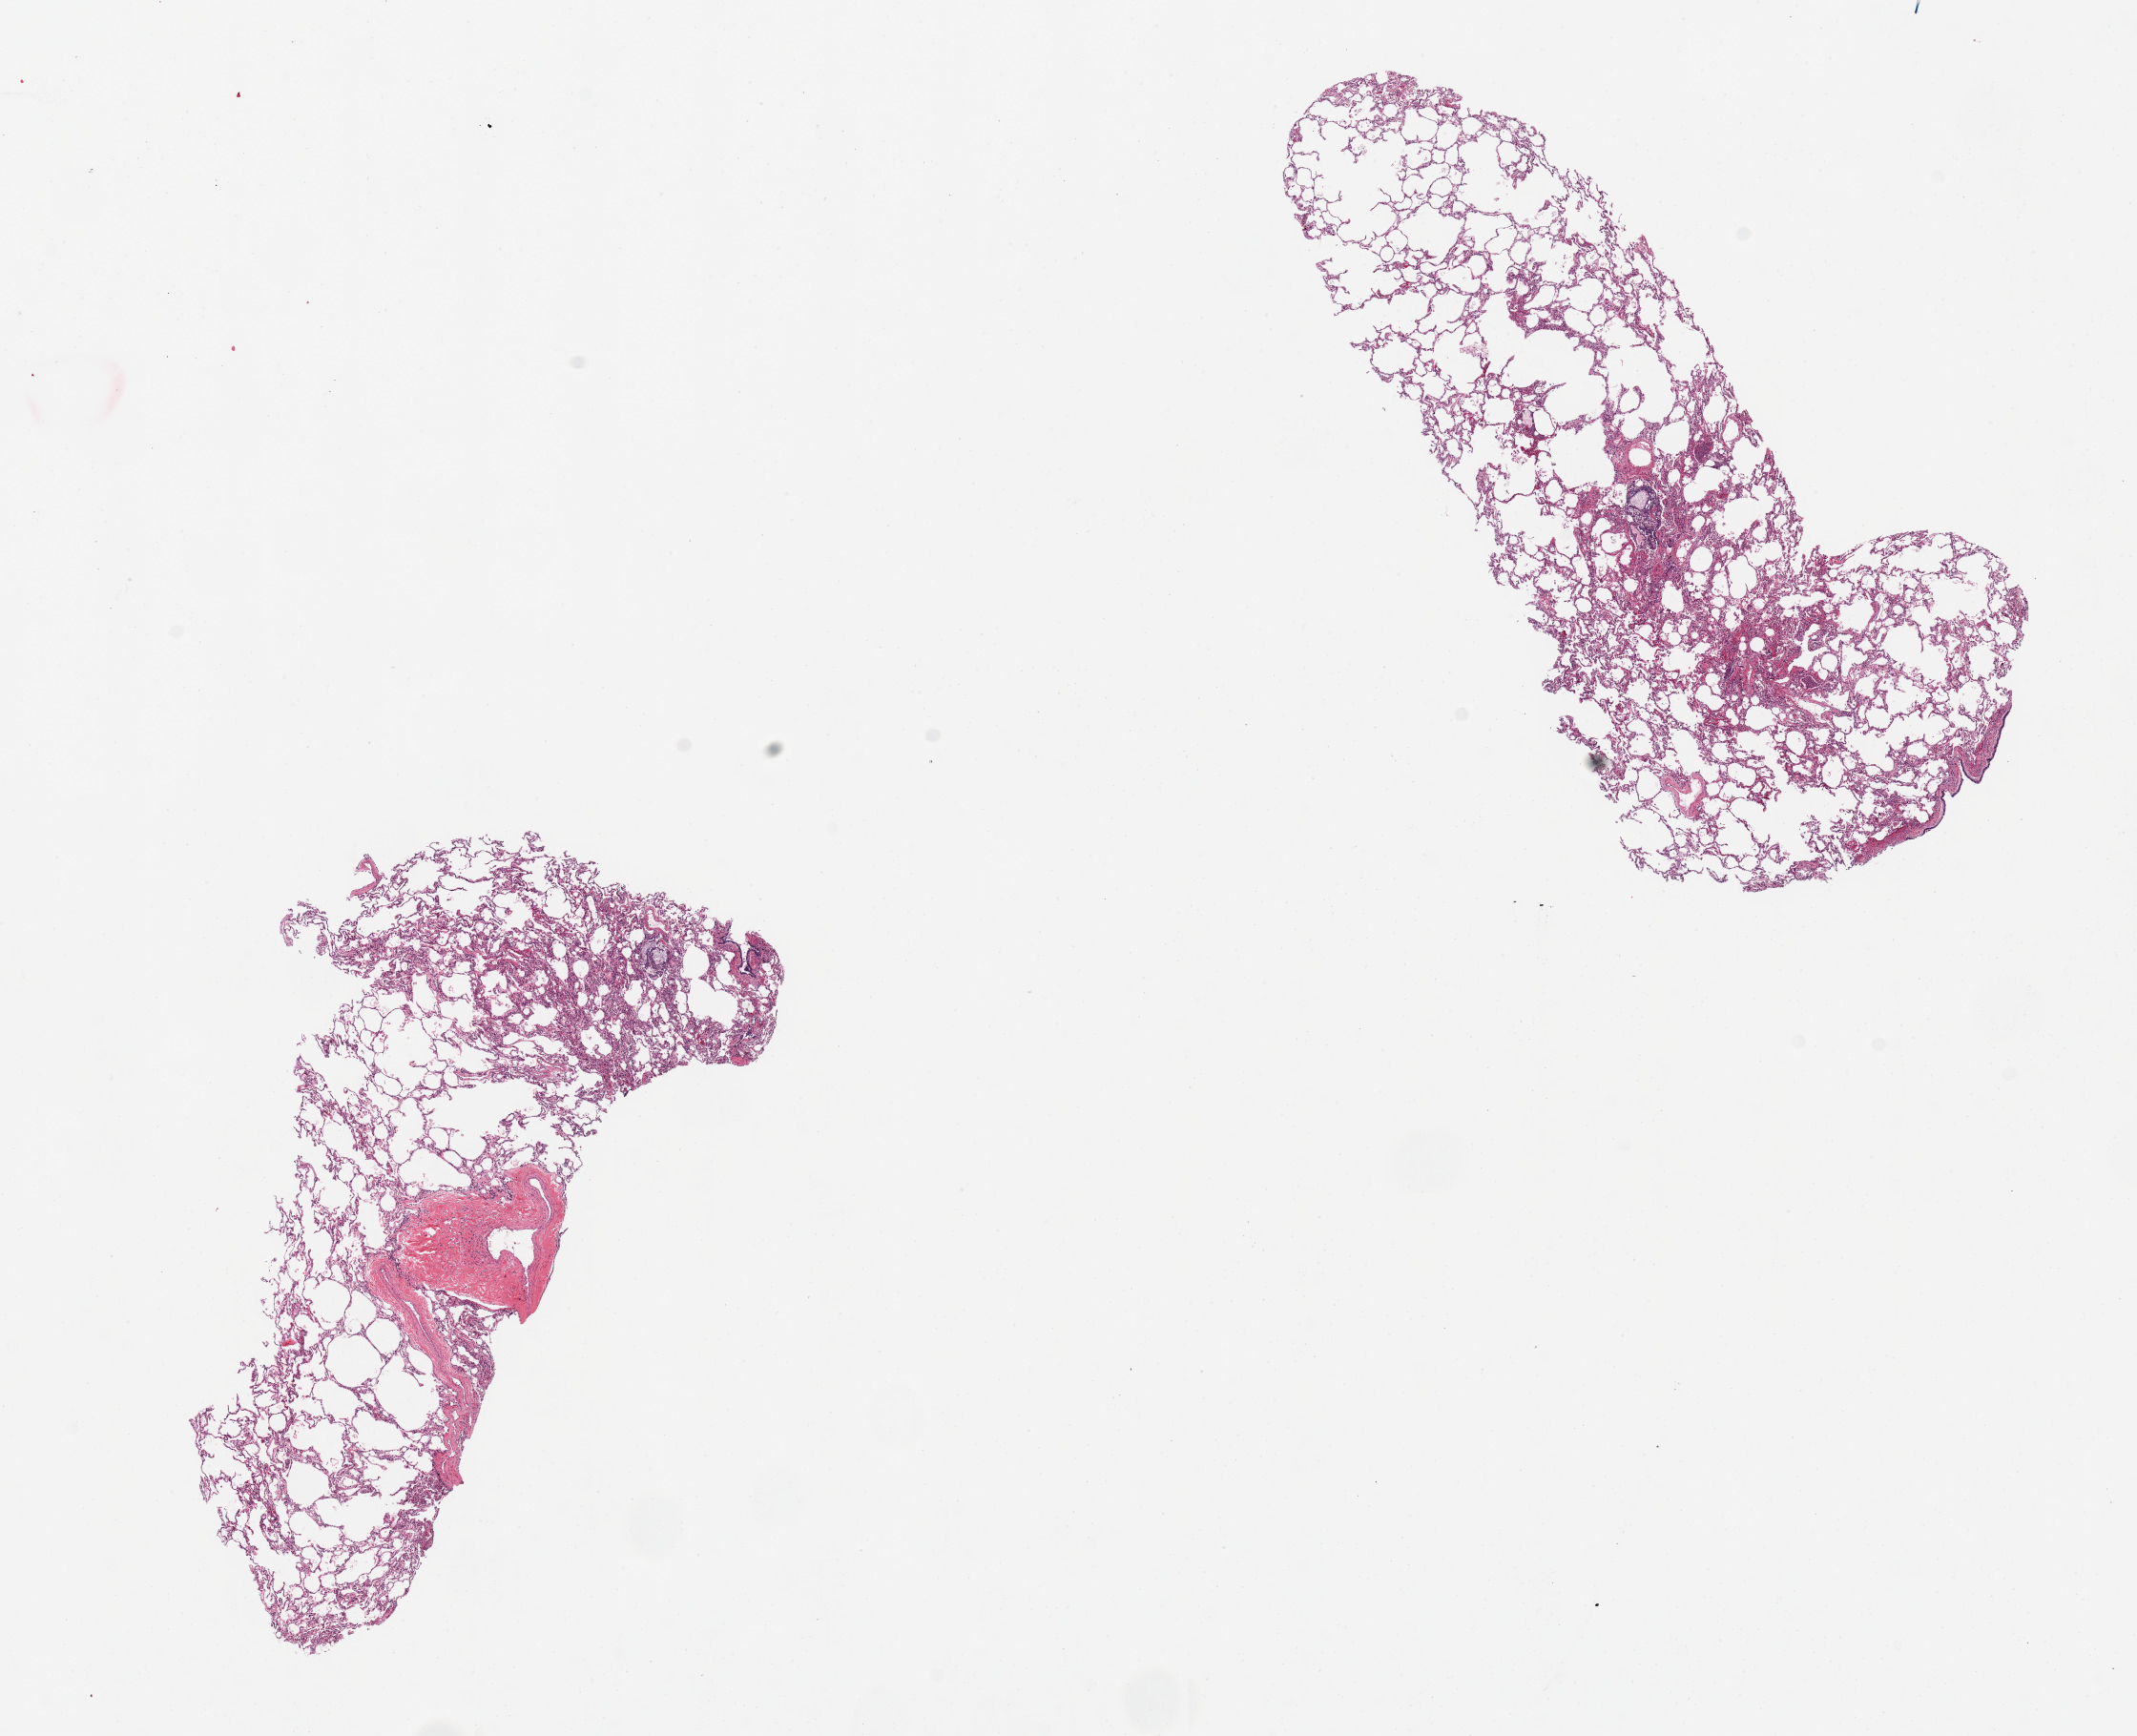
H&E whole-slide image — low-resolution overview of the scanned area, about 17.7 x 14.4 mm (slide scanned at 20x), PAXgene-fixed, paraffin-embedded tissue, sampled site (target tissue): lung, donor tissue sample. Donor: female.
- review note (as recorded): 2 pieces, patchy bronchopneumonia (?aspiration)